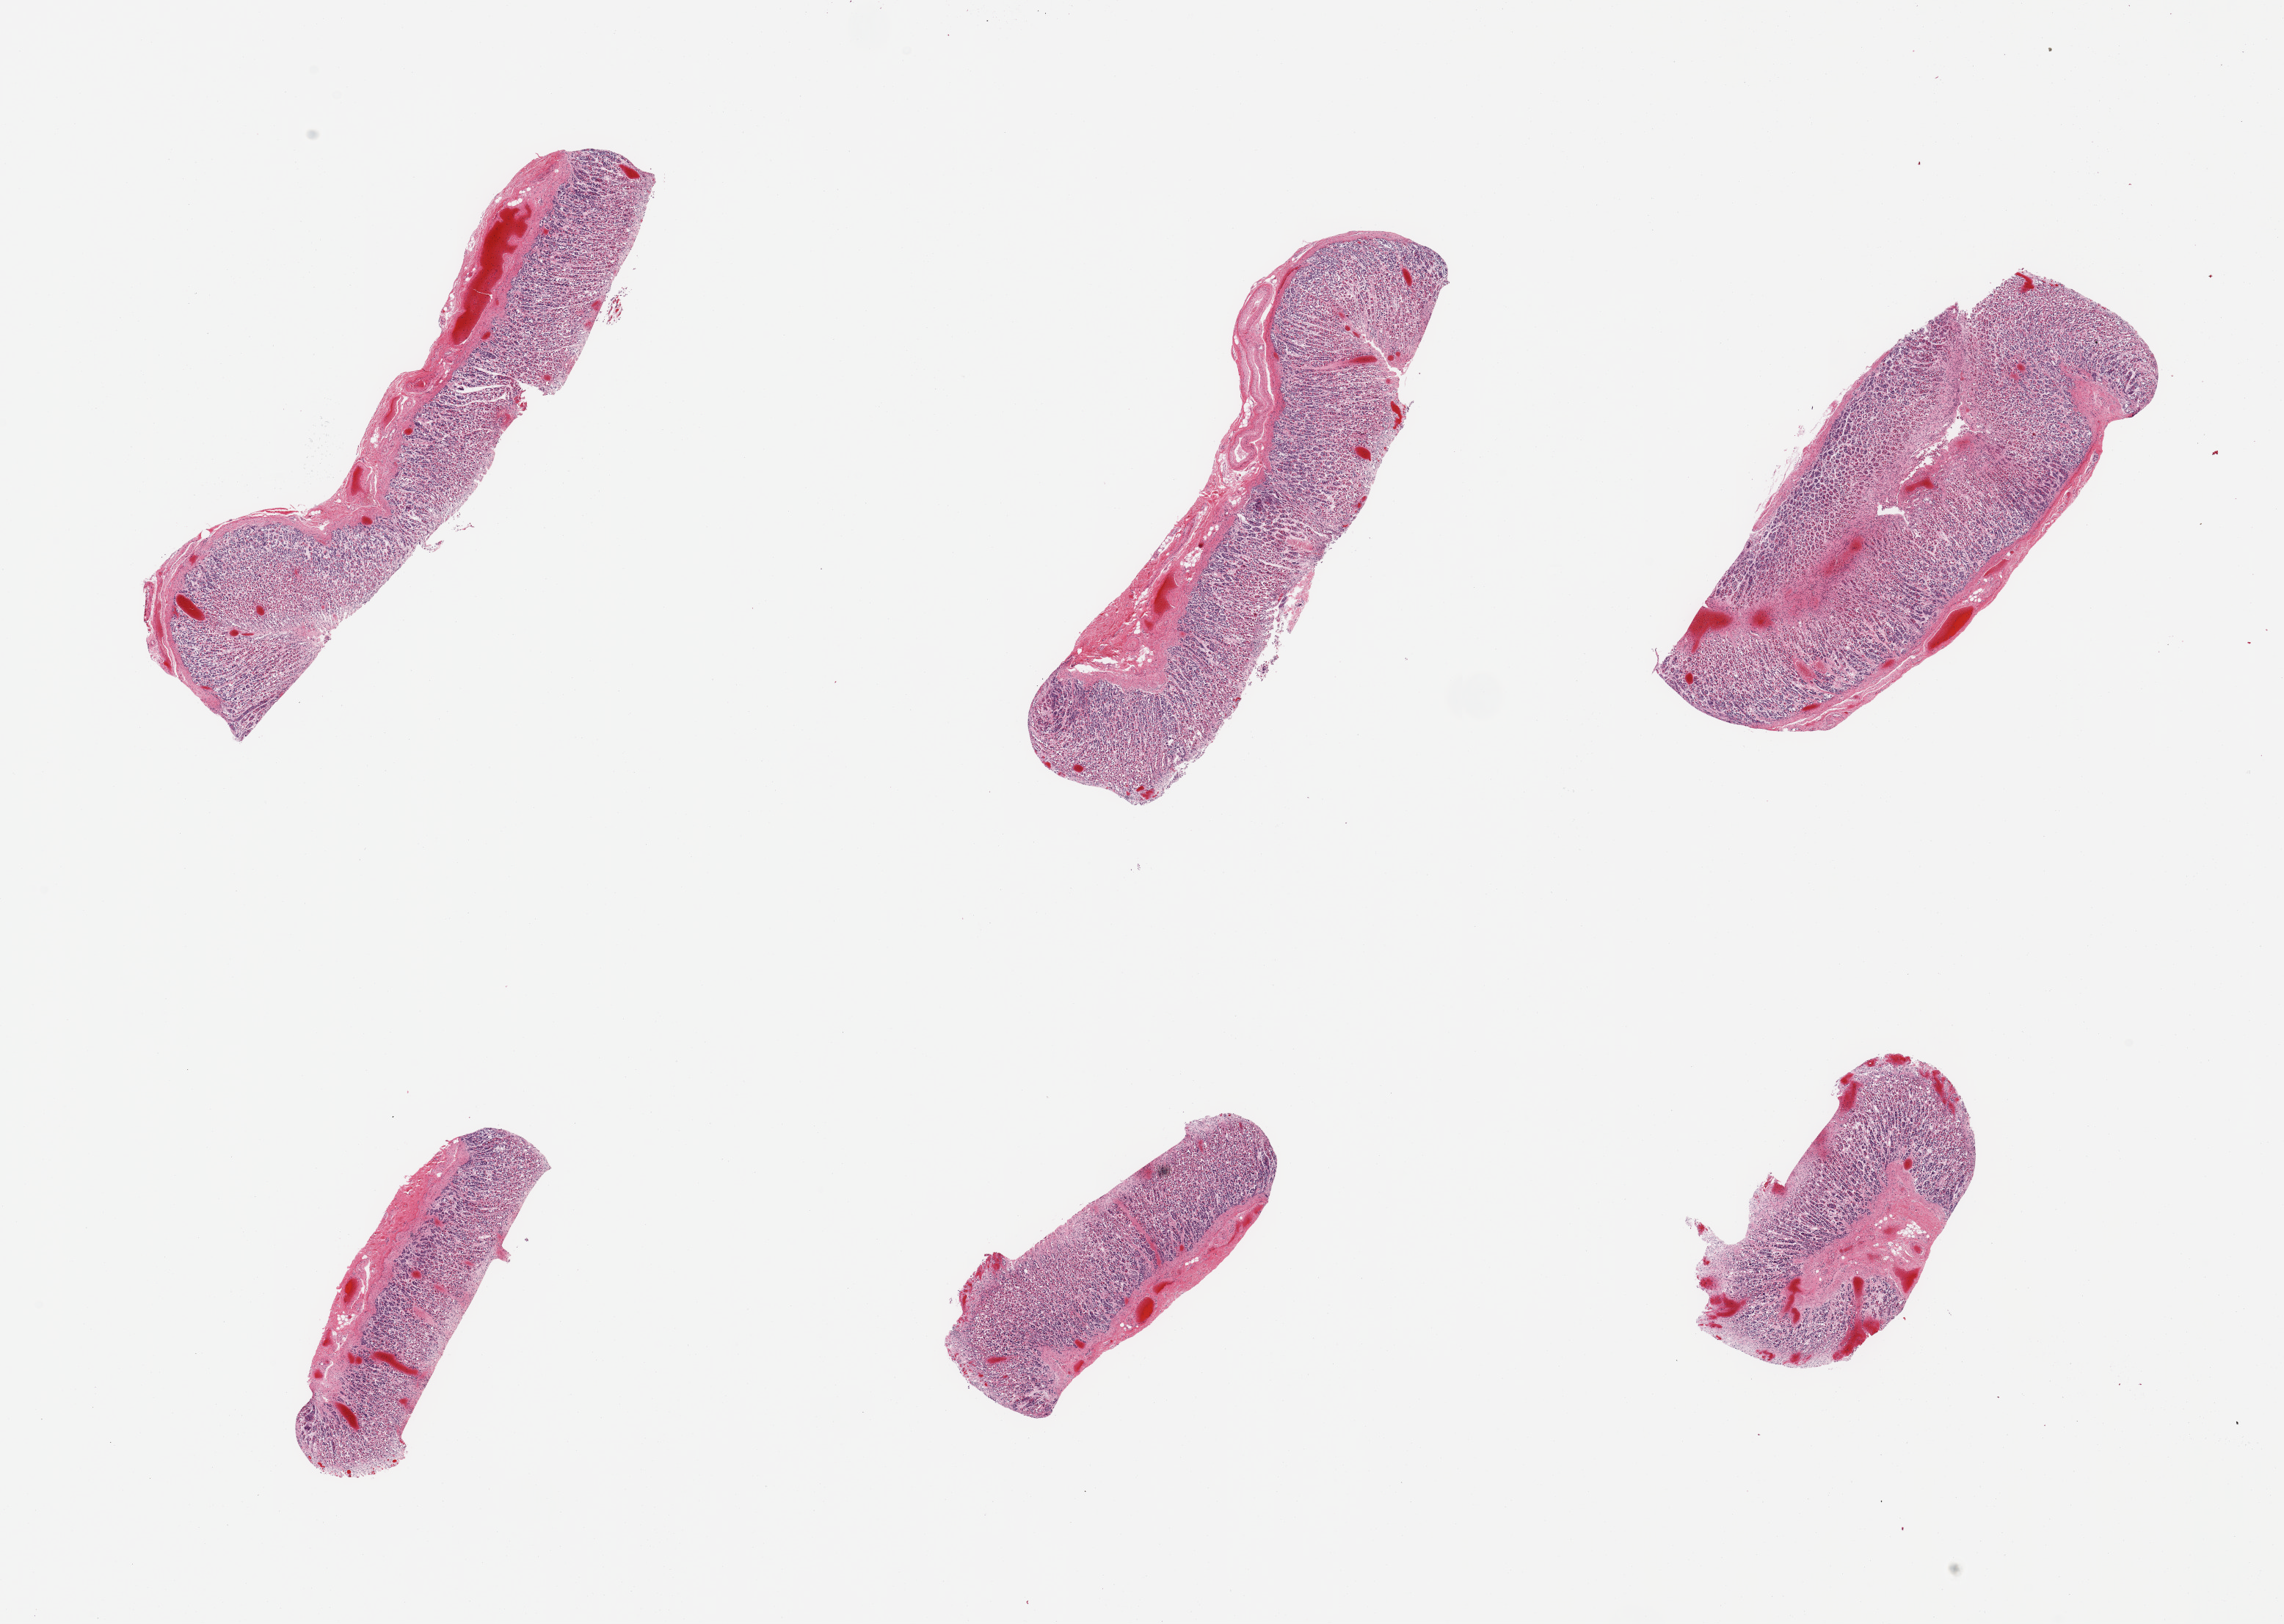
Whole-slide image, H&E stain, a low-resolution overview of the entire scanned area, about 24.6 x 17.5 mm (slide scanned at 20x); PAXgene-fixed paraffin-embedded (PFPE) section; target tissue: stomach; tissue donor sample.
Pathologist's review note for this sample: 6 pieces; mucosa only; no muscularis.